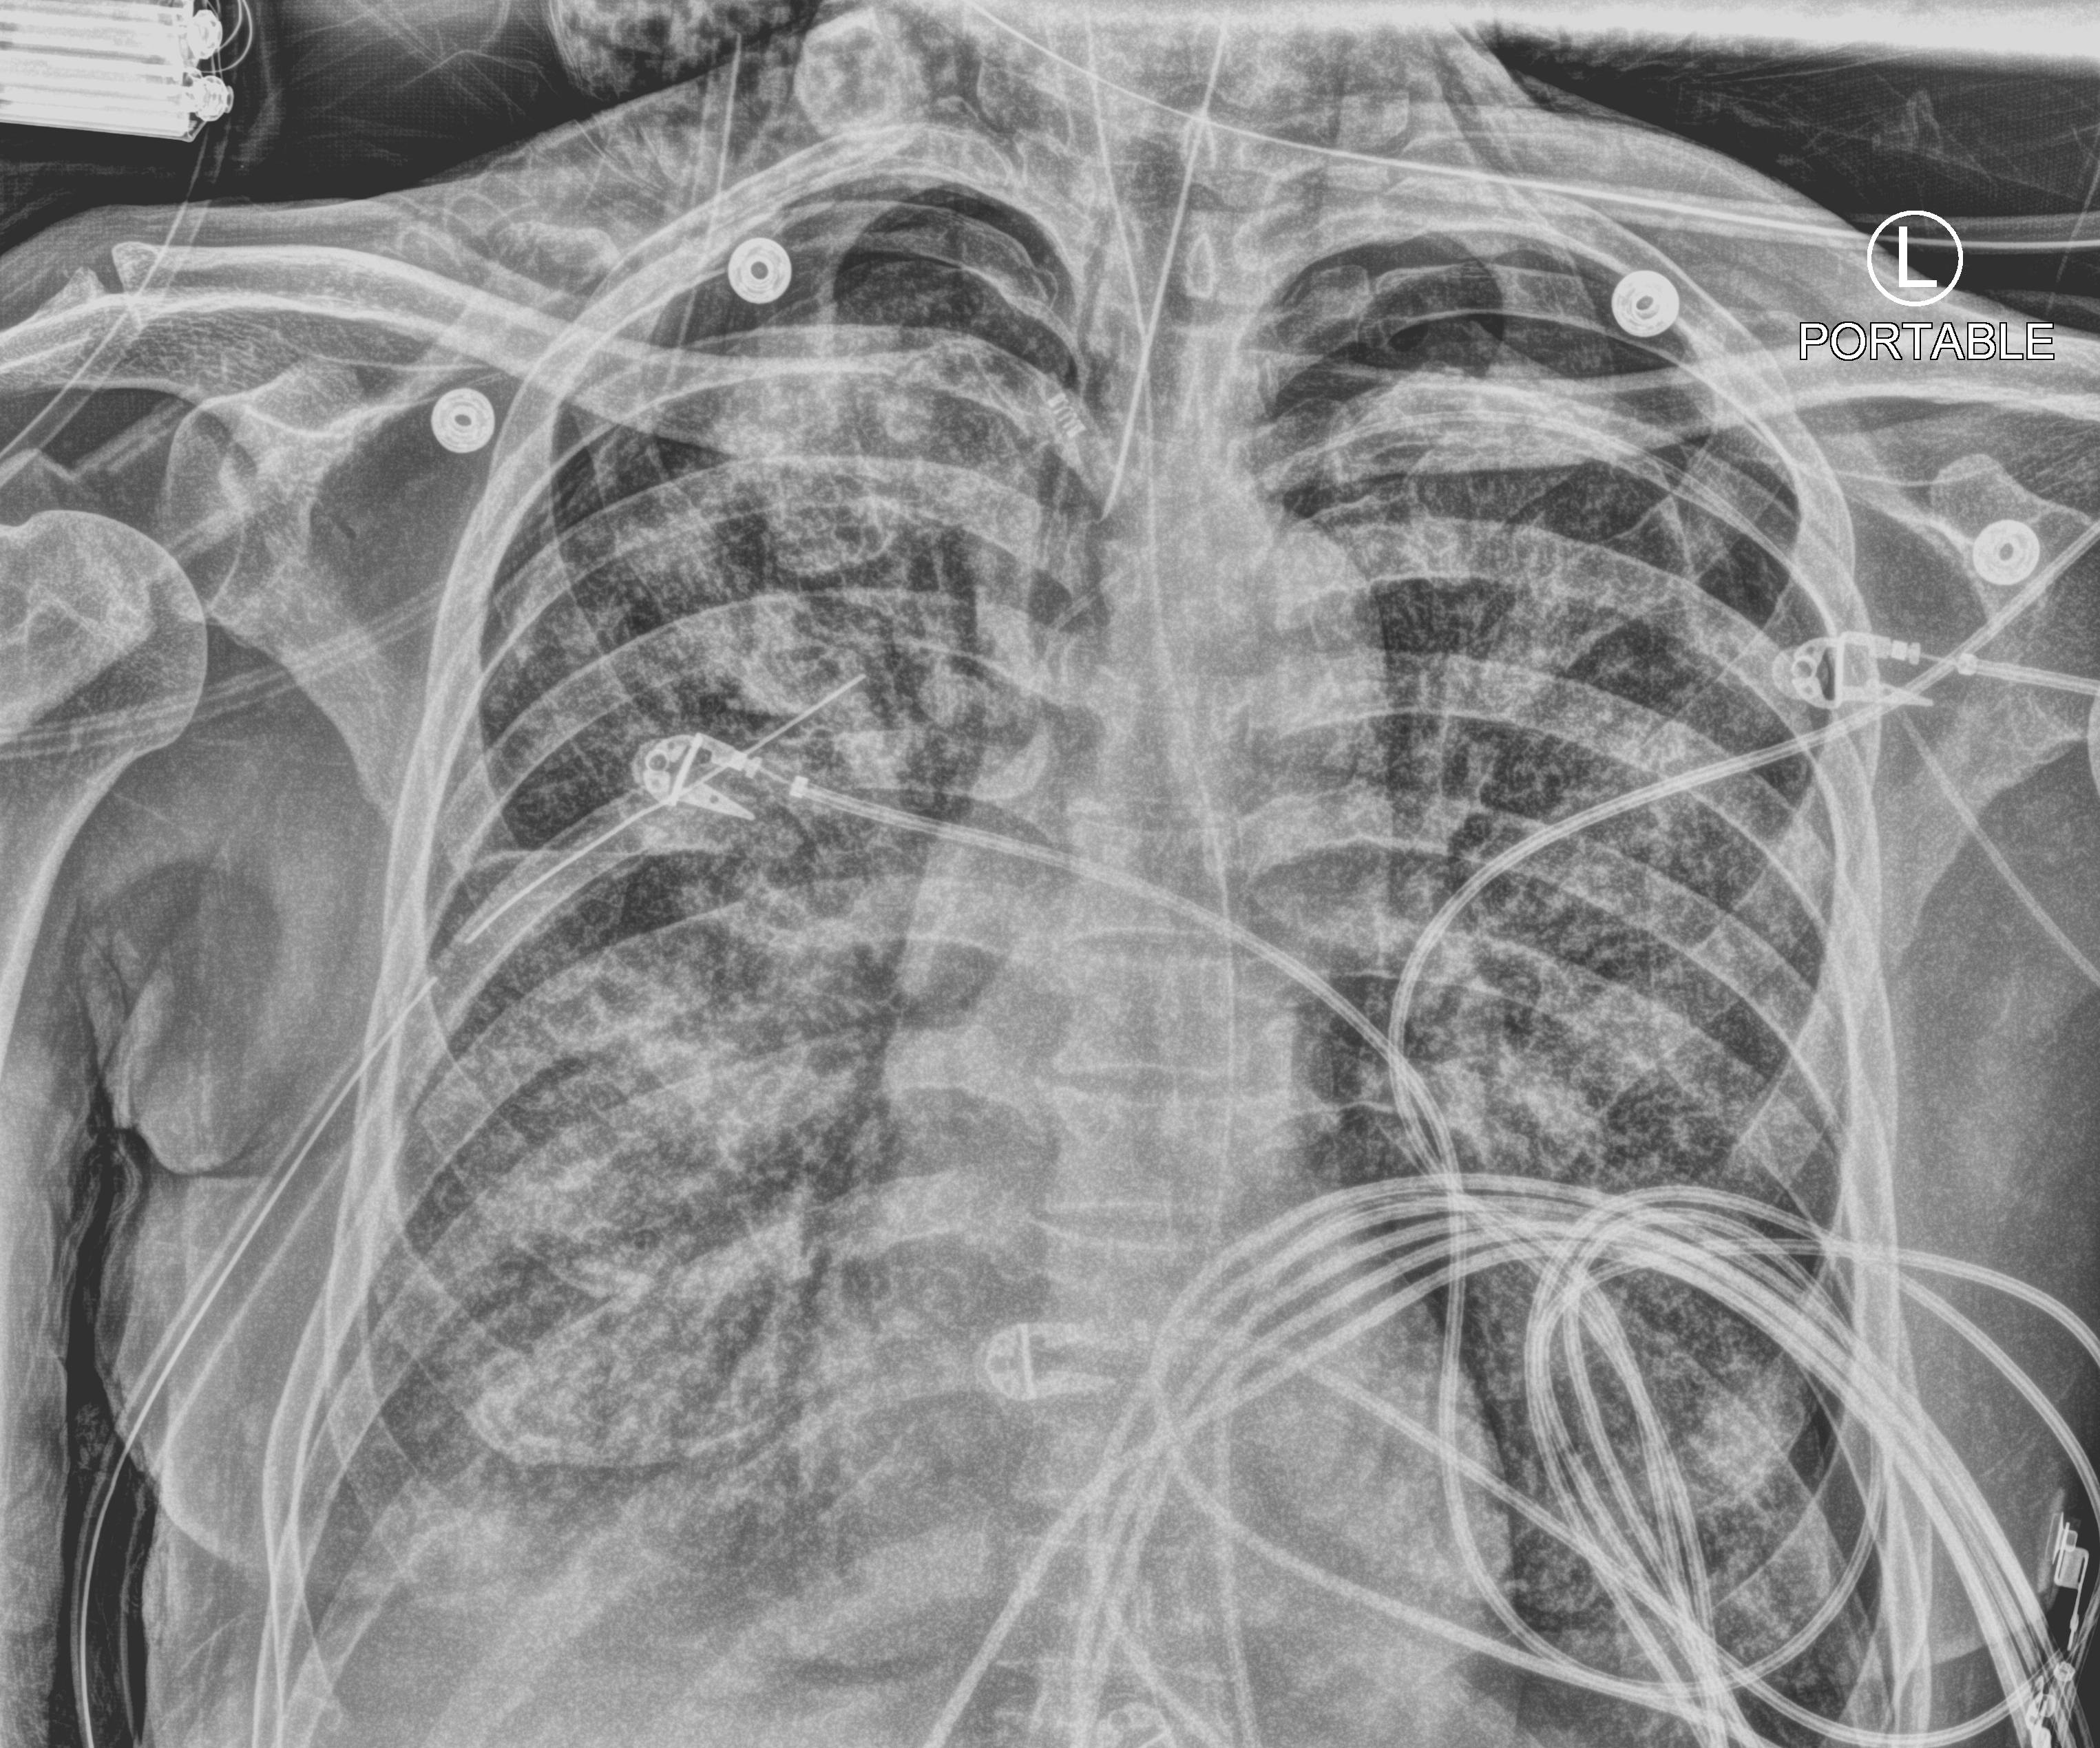
Bedside chest radiograph (computed radiography), anteroposterior (AP) projection. Male patient hospitalised with COVID-19, age 60–74 years.
Hospital-stay facts (about this admission, not read from this image; timing relative to this image not recorded):
- smoking status (admission record): former
- mechanically ventilated during this hospital stay: yes